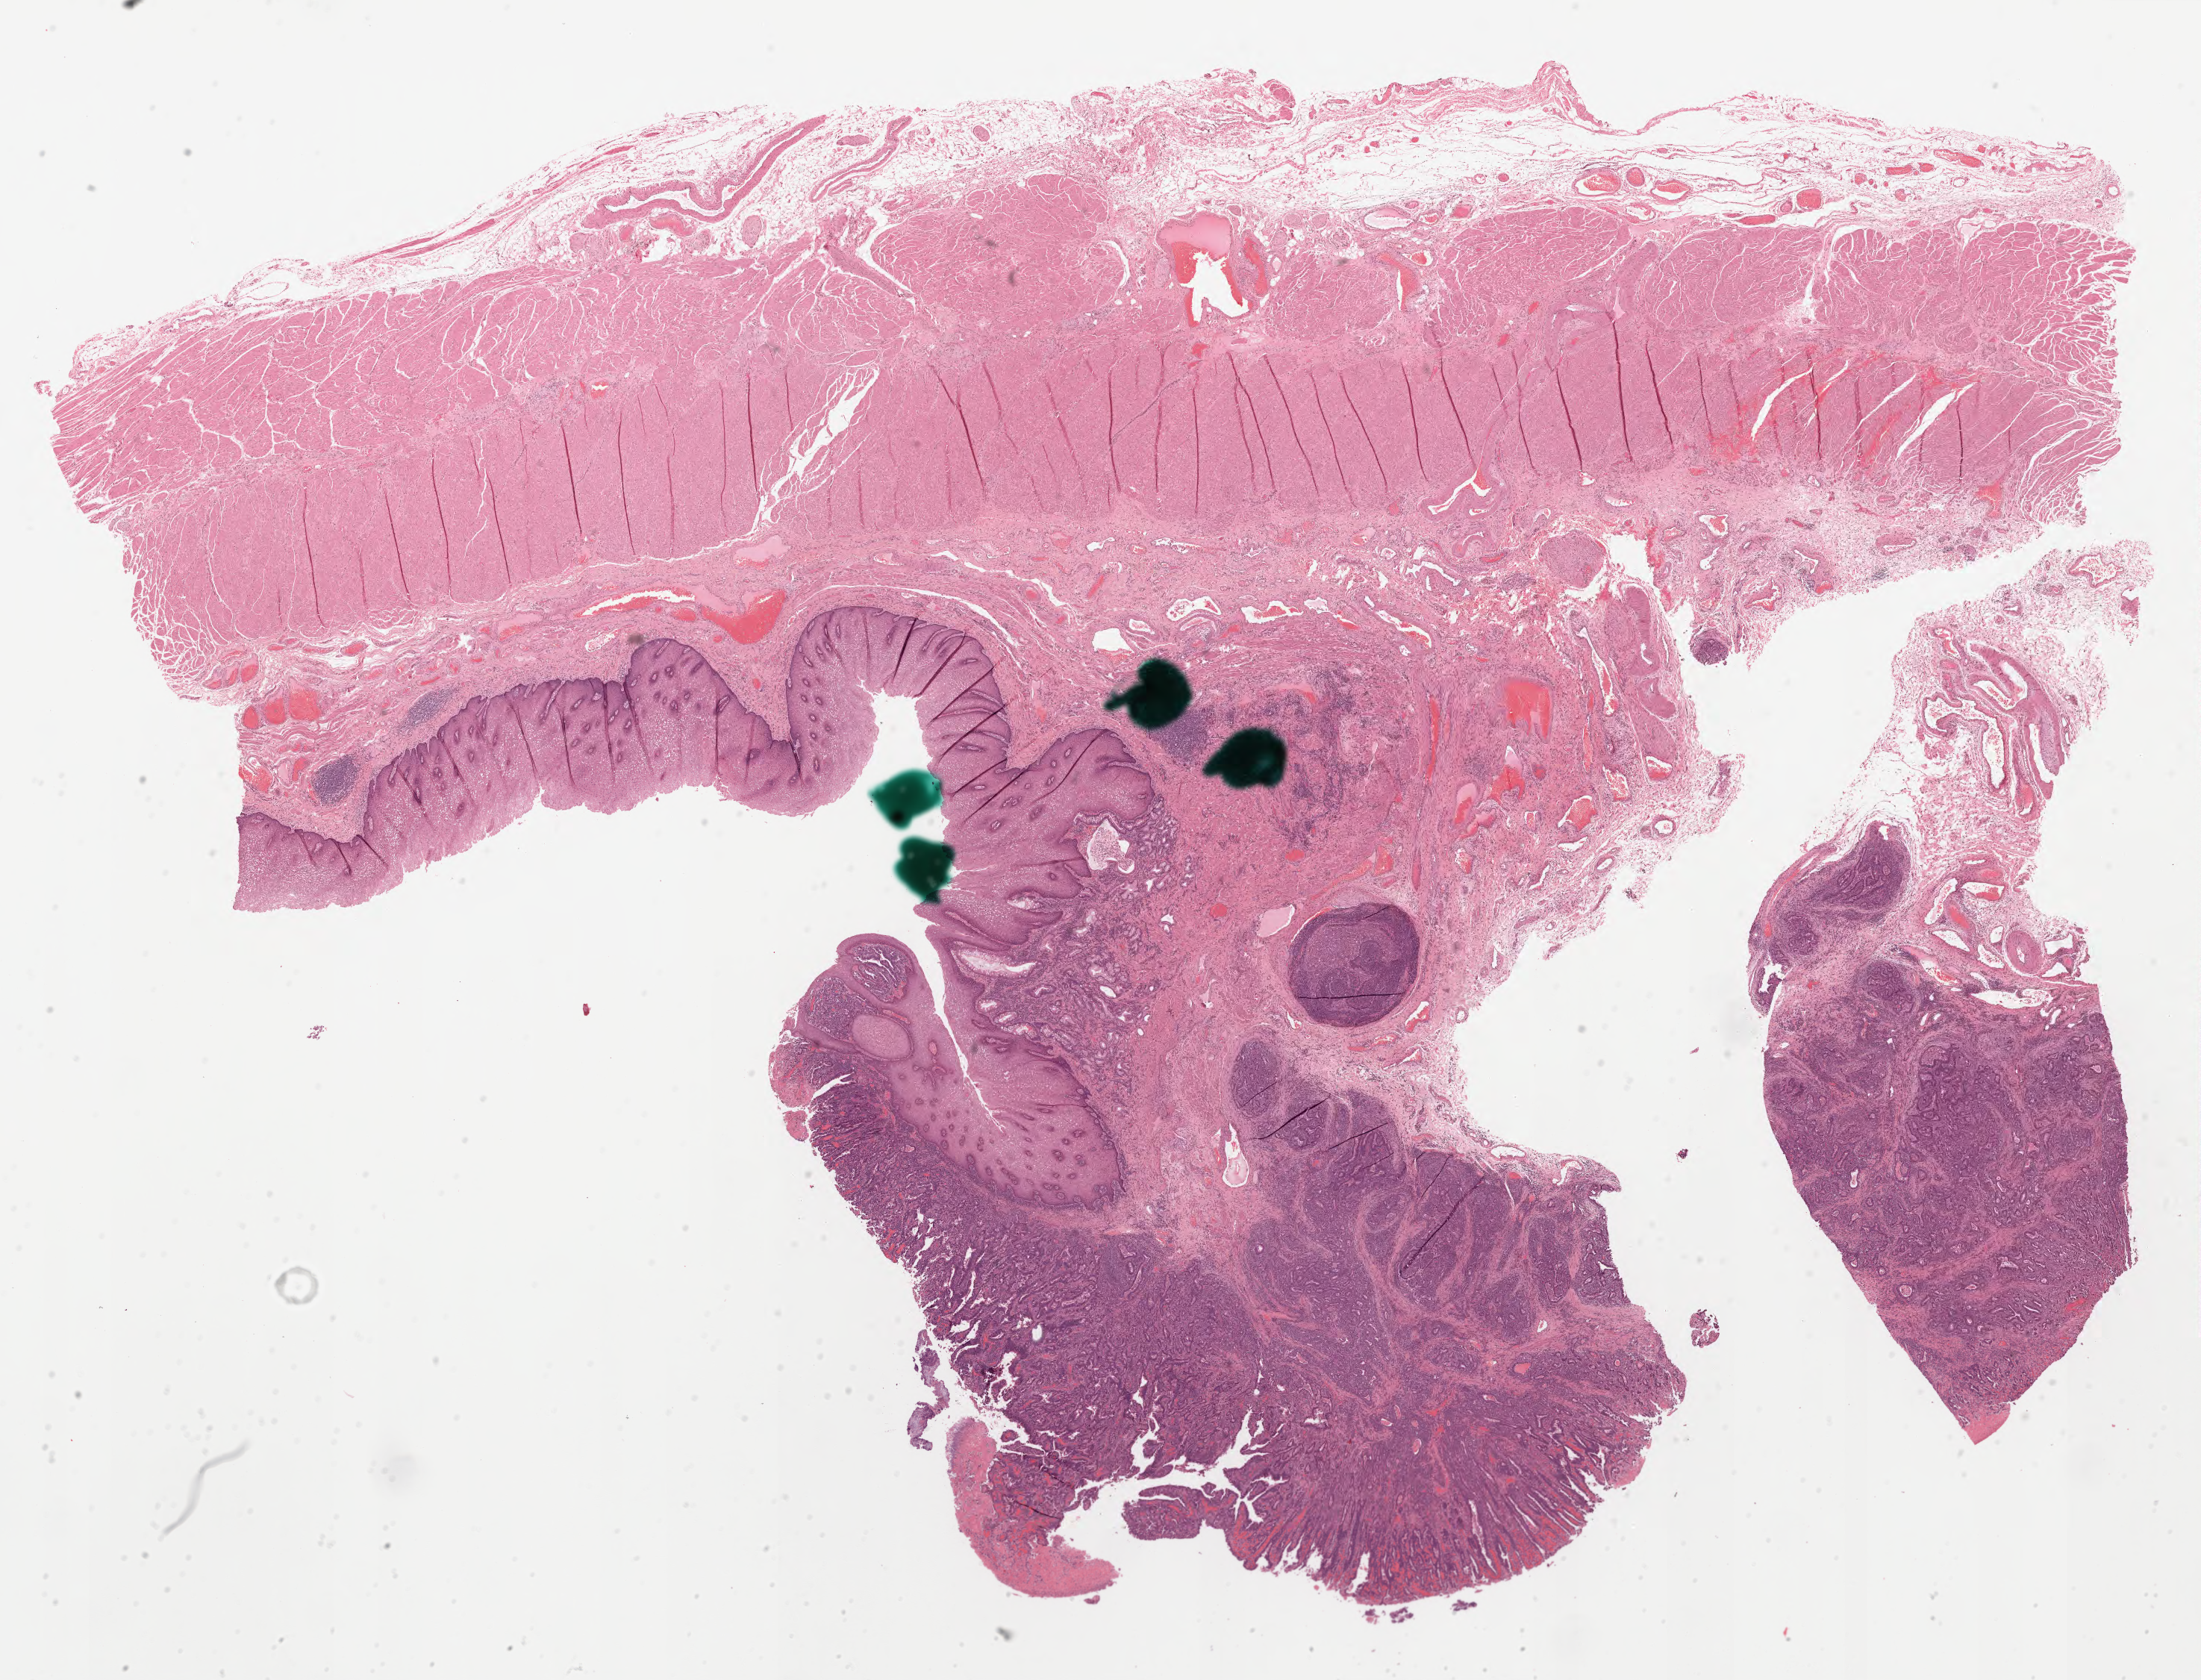
Digitized H&E tissue section (whole slide), a low-resolution overview of the entire scanned area, about 23.8 x 18.1 mm. Formalin-fixed paraffin-embedded (FFPE) diagnostic section. Esophagus, primary tumour sample. Patient: male, age at initial diagnosis 77 years. Histologic grade: G3 (poorly differentiated).
Histologic diagnosis: Adenocarcinoma, NOS (lower third of esophagus). Lymph nodes positive (case pathology): 1 of 48 examined. AJCC pathologic stage: IIB (7th edition).